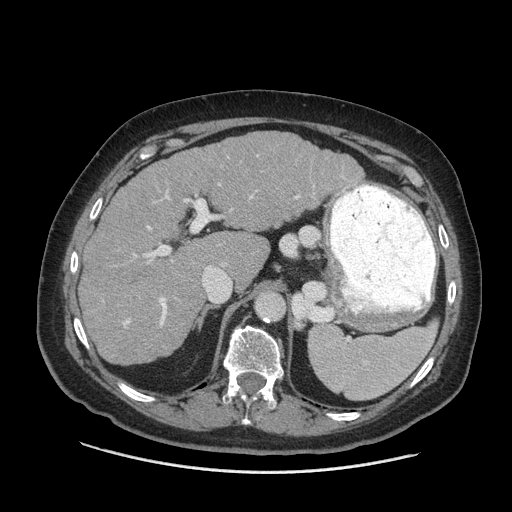
Contrast-enhanced abdominal CT (liver protocol), one axial slice; position 43 of 77 along the scan axis; reconstruction kernel STANDARD; 140 kVp; soft-tissue window (W 400 / L 40 HU); 512 × 512 image matrix, field of view 420 × 420 mm. Case-level facts recorded for this patient, not image findings: diagnosis: hepatocellular carcinoma (patient treated with transarterial chemoembolisation; whether this scan precedes or follows treatment is not stated here); TNM stage (as recorded): Stage-I.
Outlined on this slice (semi-automatically segmented with operator editing):
- liver parenchyma outside the tumour (the mass and vessels are separate outlines, so this box may not span the whole liver): box from (x=78, y=132) to (x=364, y=364) px
- liver vessels: (x=123, y=155)–(x=345, y=326)